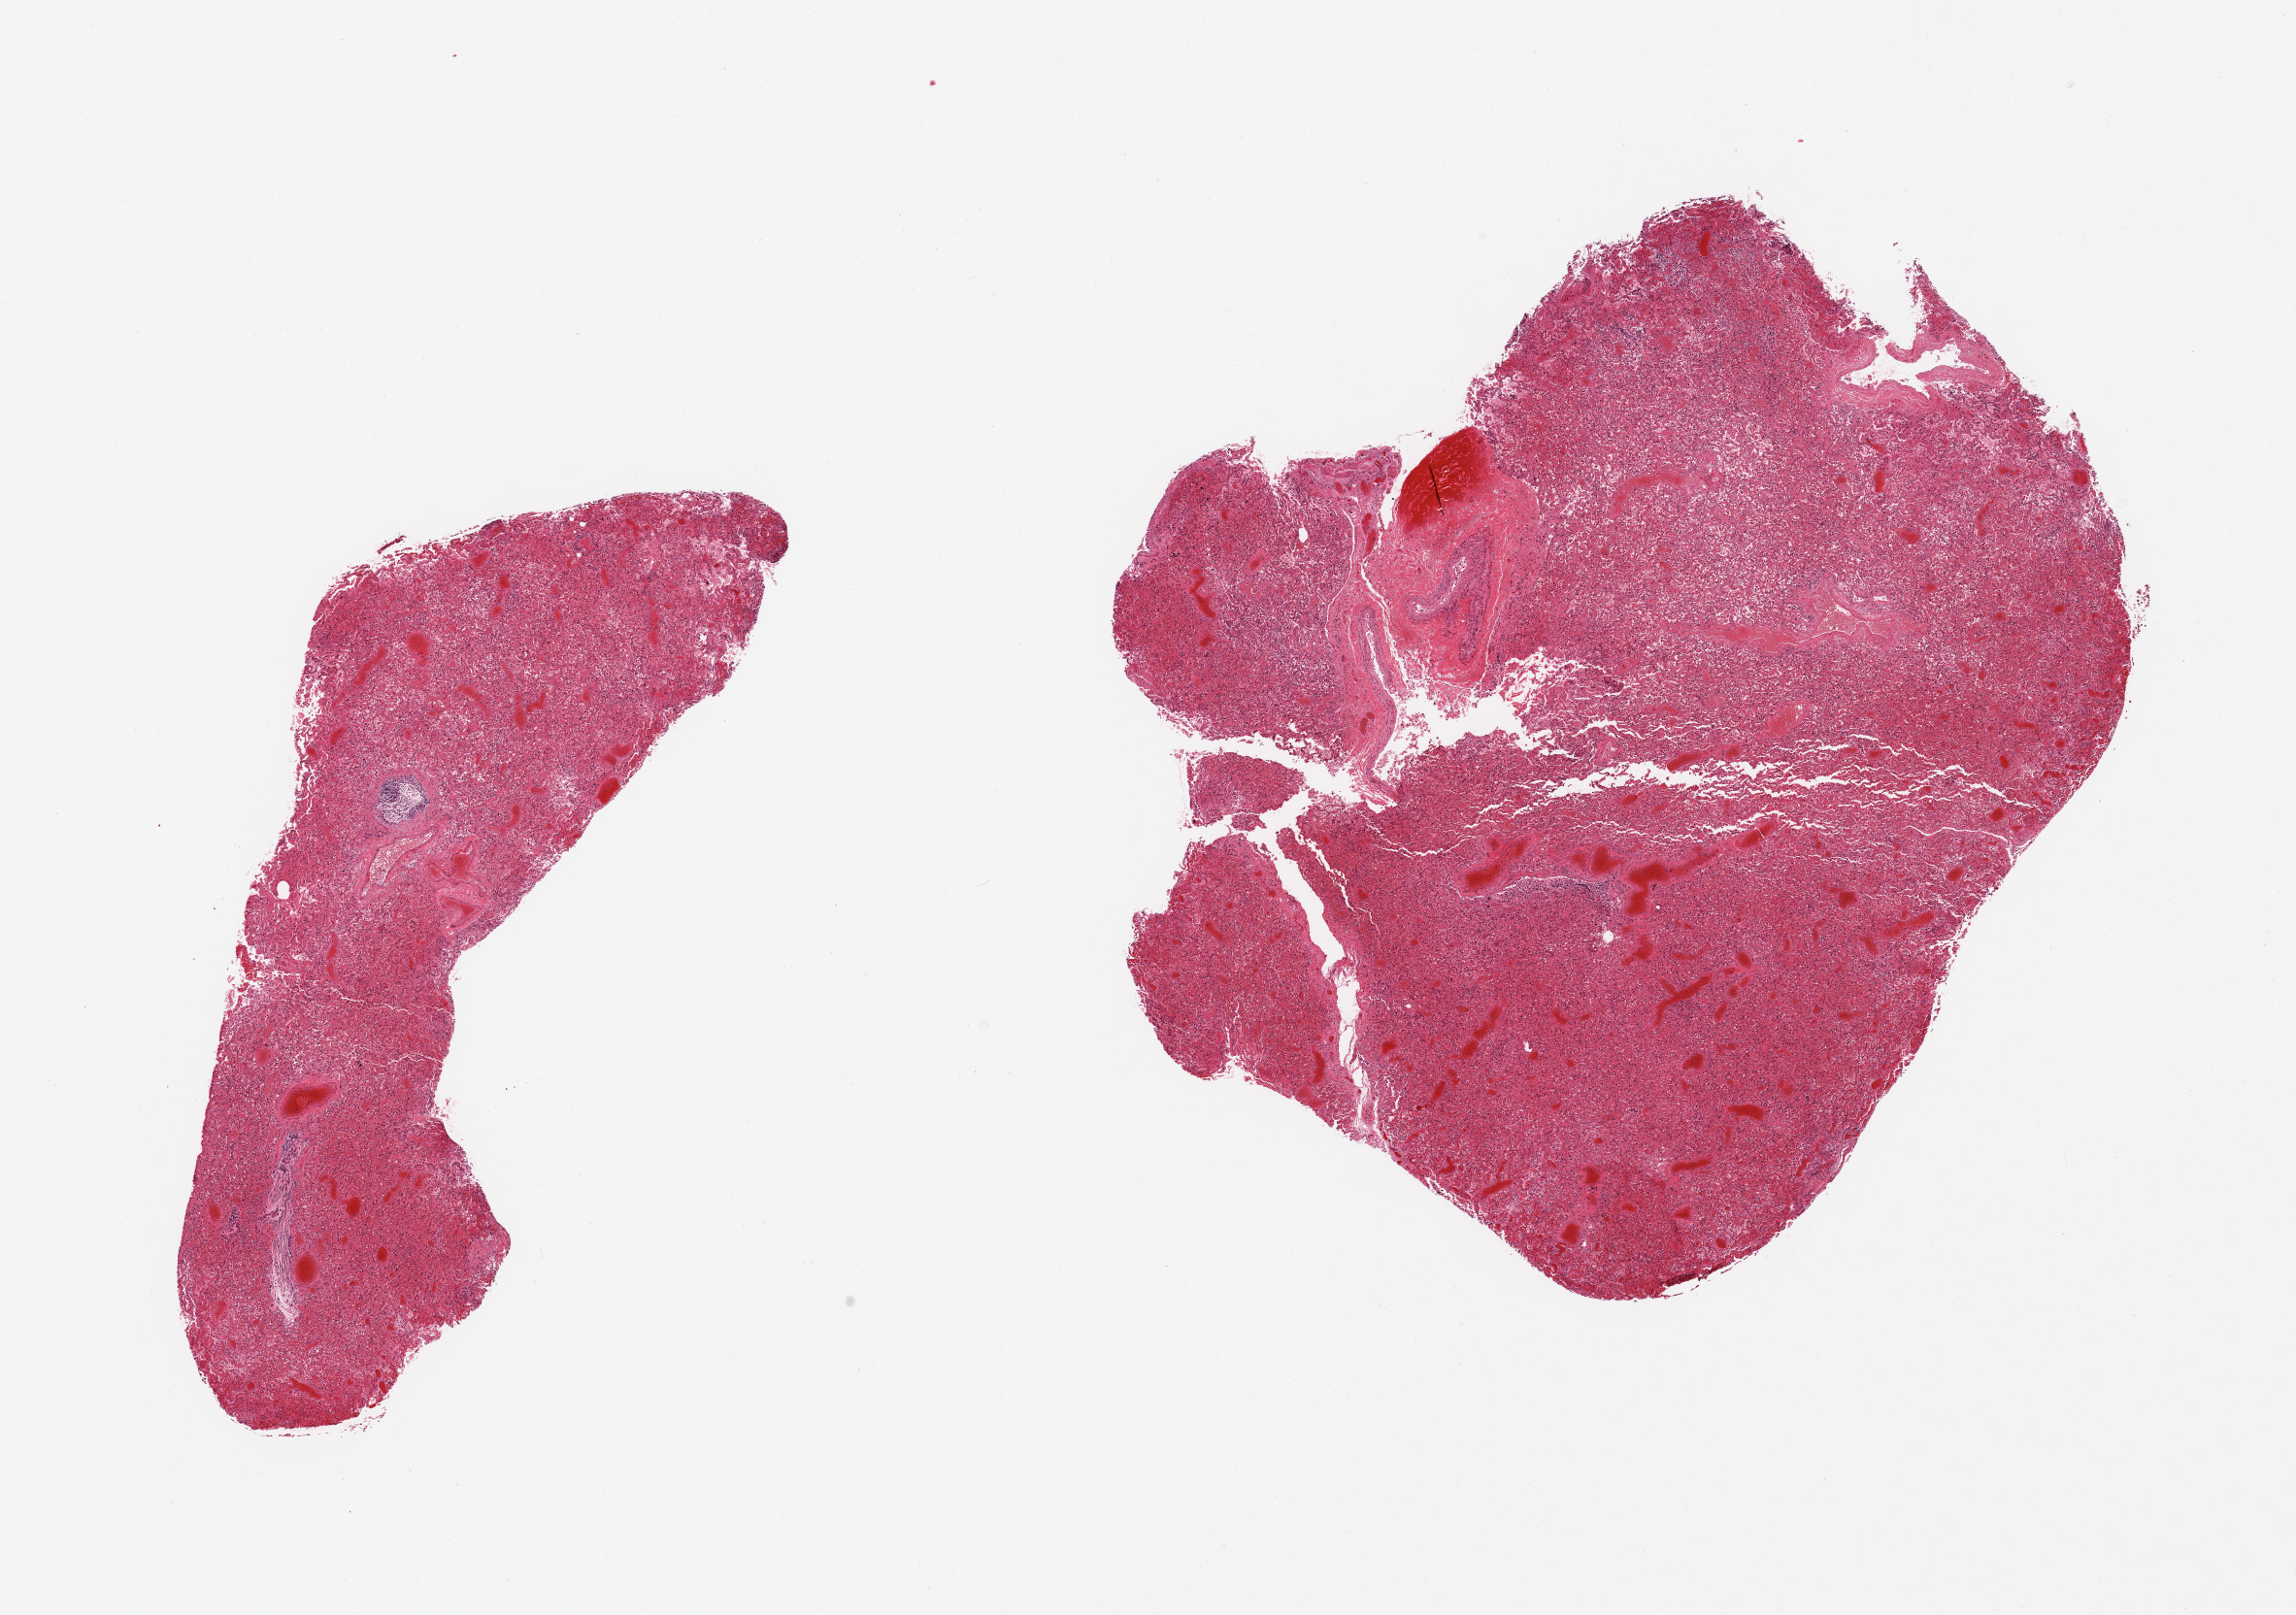
Whole-slide image, haematoxylin and eosin stain, a low-resolution overview of the entire scanned area, about 18.7 x 13.2 mm; PAXgene-fixed, paraffin-embedded tissue; section of lung (target tissue); tissue donor sample. Donor sex: female.
Reviewer comment on this tissue sample: 2 pieces; congestion and hemorrhage, patchy infiltrates.